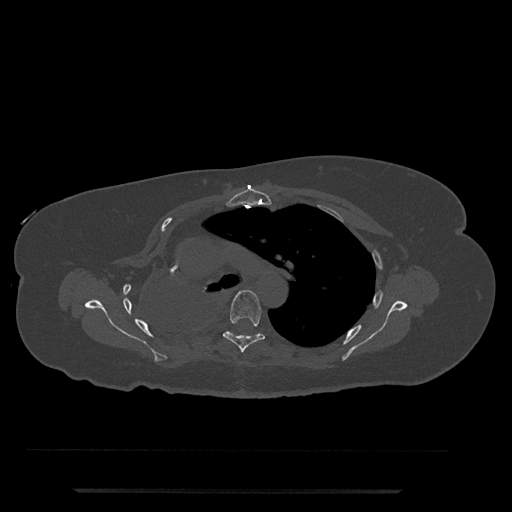
CT including the spine, one axial slice; slice 542 of 797 in the series (ordered by position); reconstruction kernel Br40s/3; 120 kVp; bone window (W 1800 / L 400 HU); 512 × 512 image matrix, field of view 440 × 440 mm. Female patient, age 51 years. From the clinical record (not read from this slice): primary cancer: neuro.
Annotated regions visible in this slice (semi-automatic segmentation, software-assisted and operator-edited):
- T5 vertebra: bounding box [x1, y1, x2, y2] px = [223, 290, 265, 353]